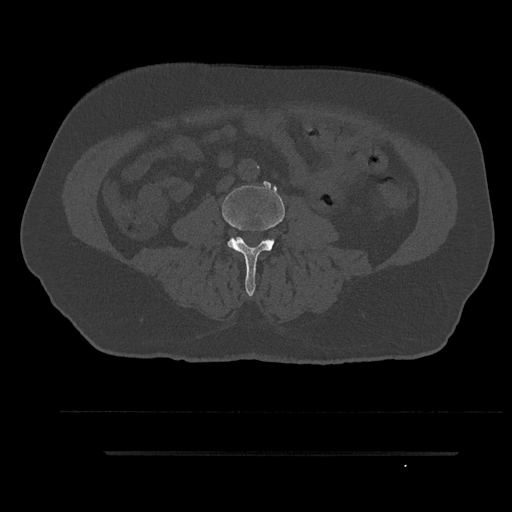
CT including the spine, one axial slice; slice 28 of 797 in the series (ordered by position); reconstruction kernel Br40s/3; bone window (W 1800 / L 400 HU); 0.5 mm slice thickness; 512 × 512 image matrix, field of view 432 × 432 mm. Male patient, age 63 years. From the clinical record (not read from this slice): primary cancer: renal; vertebrae with lytic lesions (as recorded): T8.
Annotated regions visible in this slice (semi-automatic segmentation, software-assisted and operator-edited):
- L3 vertebra: box from (x=222, y=185) to (x=285, y=296) px
- L4 vertebra: (x=267, y=239)–(x=274, y=245)